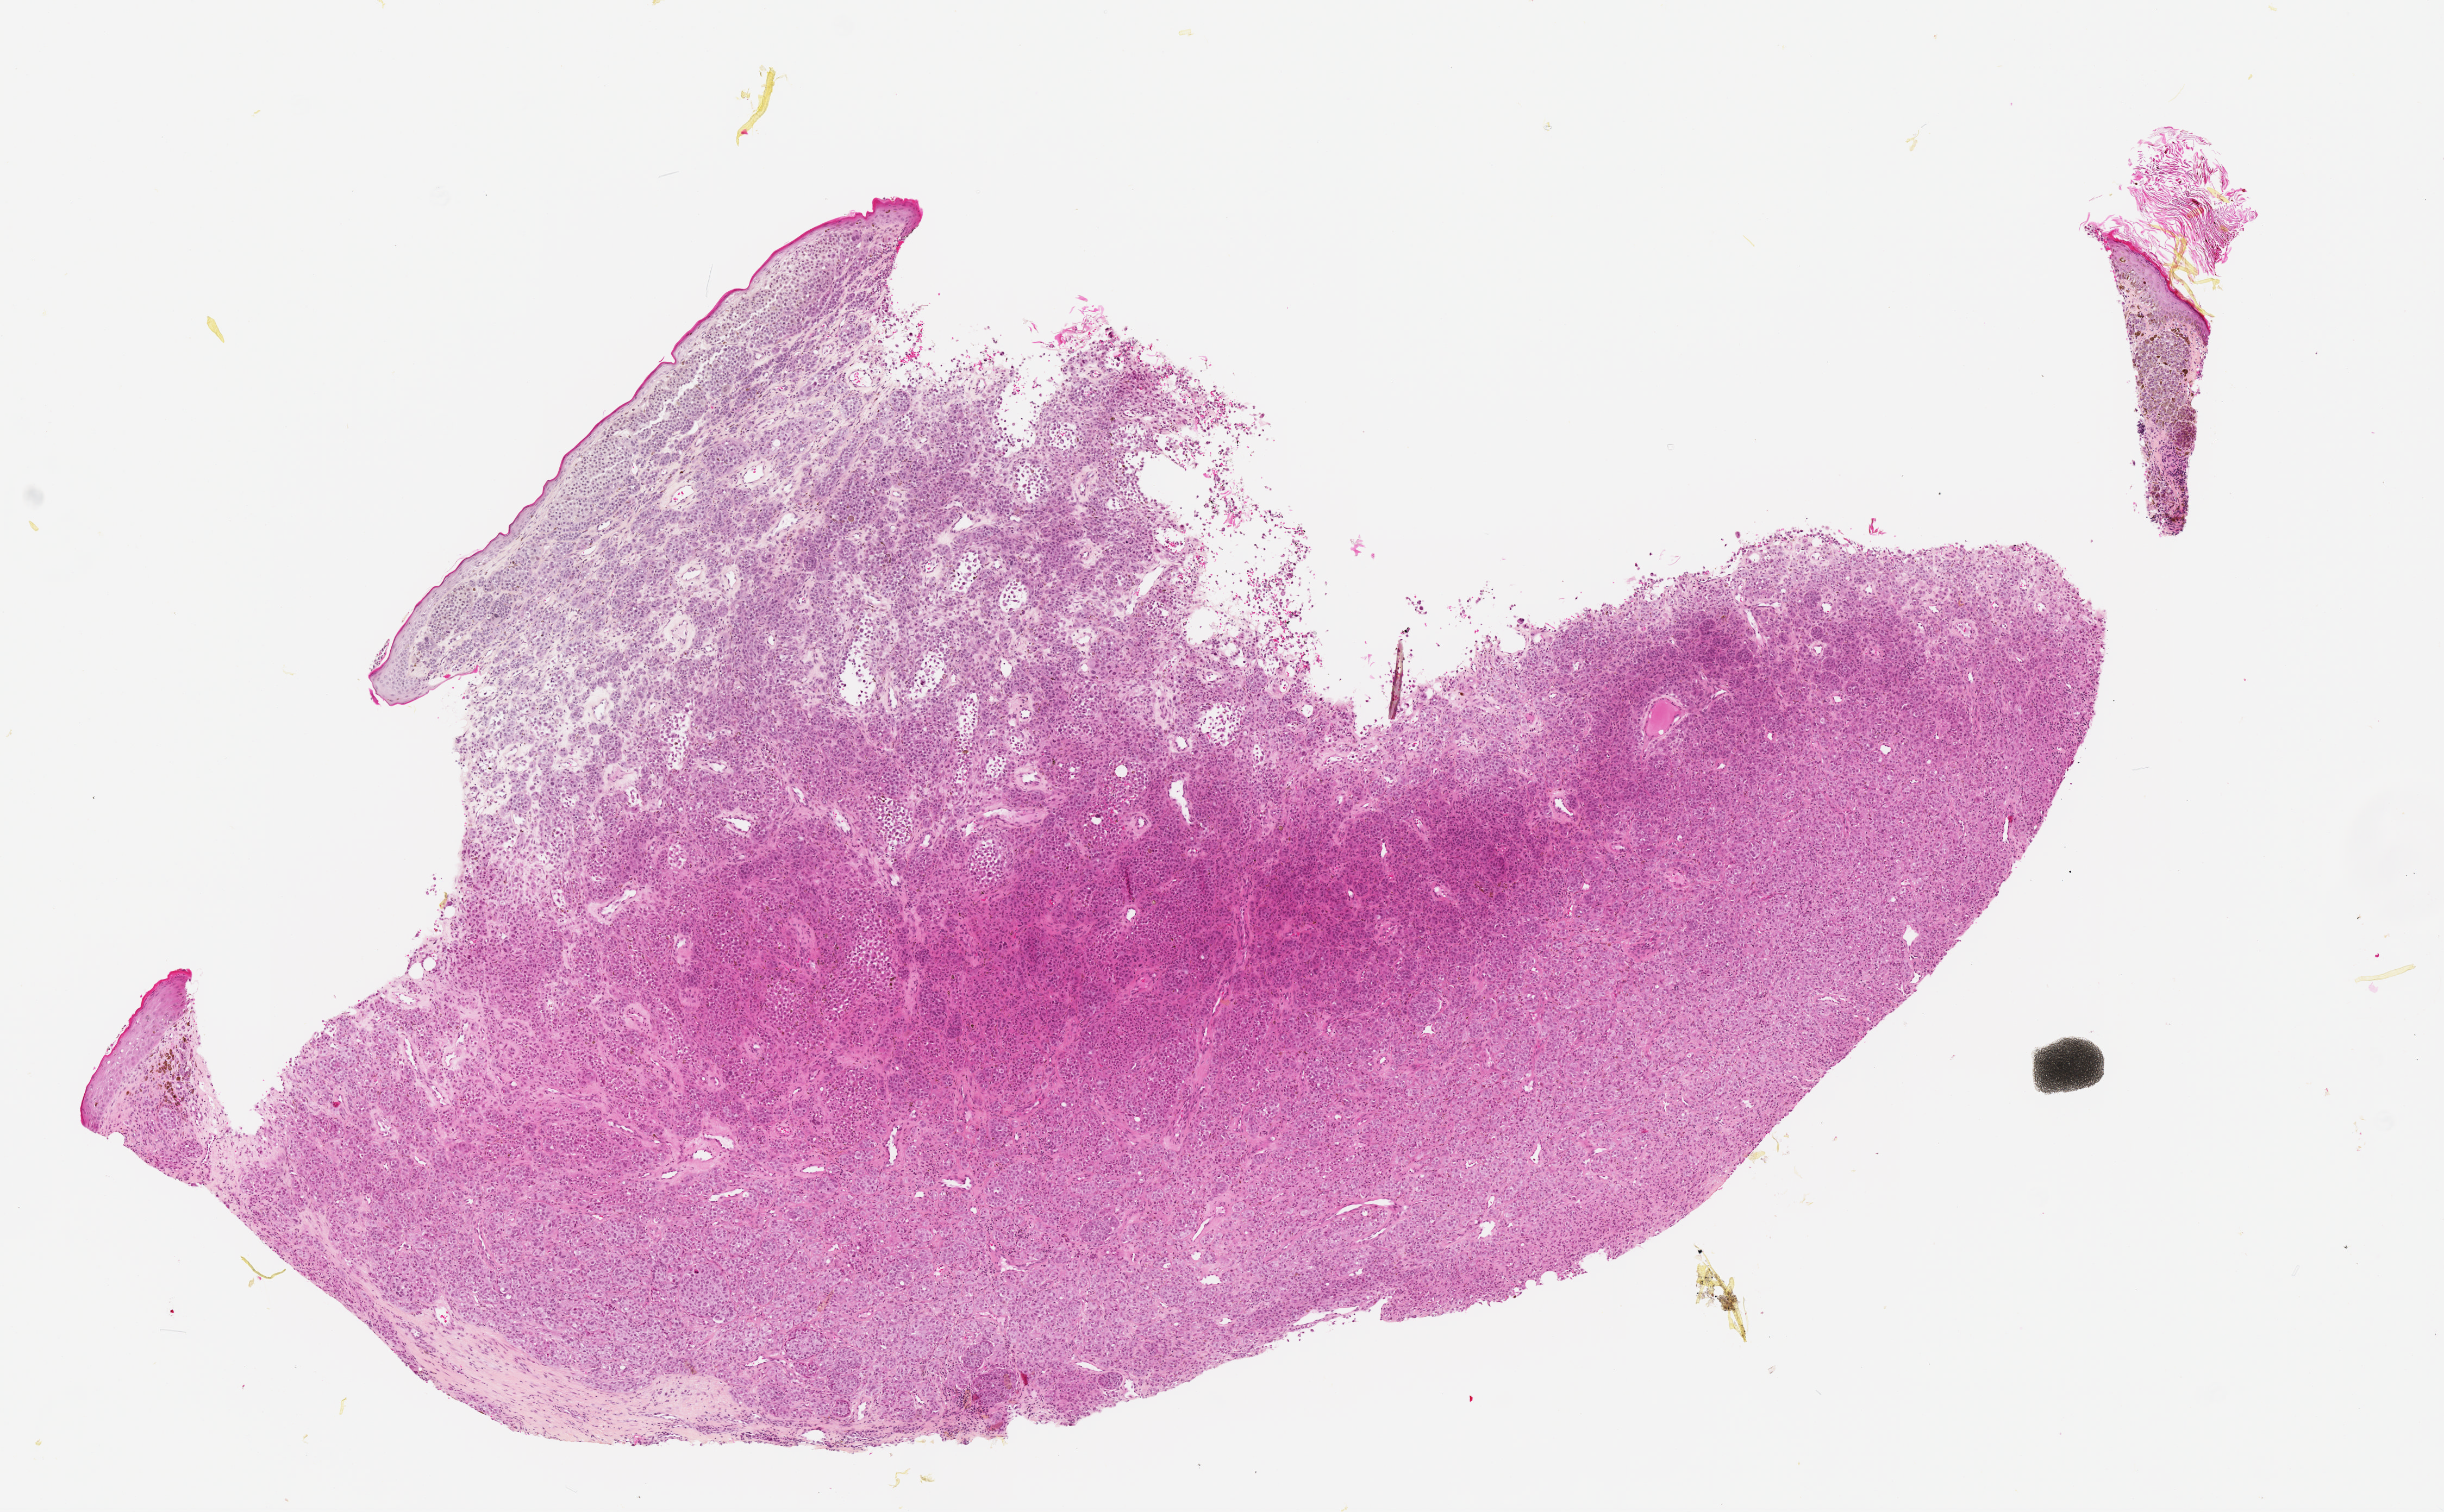
Digitized H&E-stained tissue section (whole slide) — shown as a low-resolution overview of the whole scanned area (about 9.0 x 5.6 mm, from a 20x scan). FFPE section. Skin, primary tumour sample. Patient sex: female.
Histologic diagnosis: Malignant melanoma, NOS.